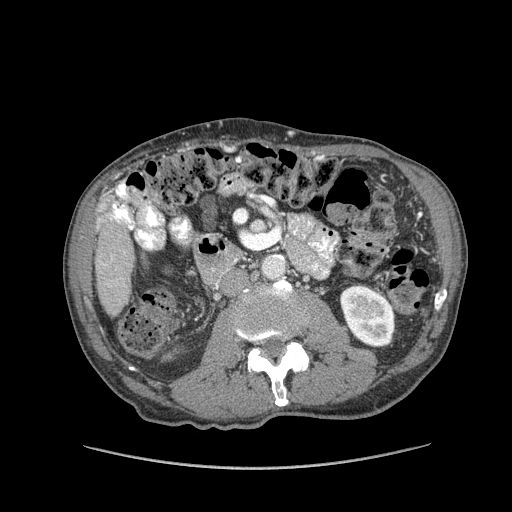
Contrast-enhanced abdominal CT (liver protocol), one axial slice. Slice 17 of 162 in the series (ordered by position). 100 kVp. Soft-tissue window (W 400 / L 40 HU). 2.5 mm slice thickness. 512 × 512 image matrix, field of view 400 × 400 mm. From the clinical record (not read from this slice): diagnosis: hepatocellular carcinoma (patient treated with transarterial chemoembolisation; whether this scan precedes or follows treatment is not stated here); TNM stage (as recorded): Stage-IIIA; Child-Pugh class: A; tumour nodularity: multinodular; tumour size: 9.9 cm.
Structures marked on this image (semi-automatic segmentation, software-assisted and operator-edited):
- liver parenchyma outside the tumour (the mass and vessels are separate outlines, so this box may not span the whole liver): box from (x=94, y=192) to (x=134, y=316) px
- liver vessels: (x=111, y=204)–(x=120, y=223)